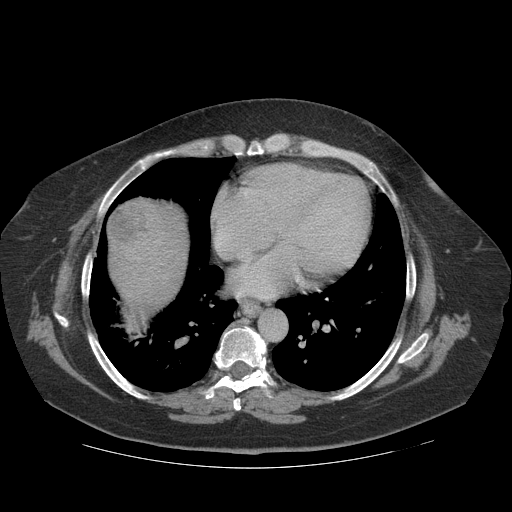
Contrast-enhanced abdominal CT (liver protocol), one axial slice. Slice 109 of 121 in the series (ordered by position). Reconstruction kernel STANDARD. 140 kVp. Soft-tissue window (W 400 / L 40 HU). 2.5 mm slice thickness. 512 × 512 image matrix. From the clinical record (not read from this slice): diagnosis: hepatocellular carcinoma (patient treated with transarterial chemoembolisation; whether this scan precedes or follows treatment is not stated here); TNM stage (as recorded): Stage-IIIA; Child-Pugh class: A; tumour differentiation: well differentiated; tumour nodularity: multinodular.
Annotated regions visible in this slice (semi-automatic segmentation, software-assisted and operator-edited):
- liver parenchyma outside the tumour (the mass and vessels are separate outlines, so this box may not span the whole liver): bounding box <108,196,188,314> (left, top, right, bottom; pixels)
- mass: <108,208,143,242>